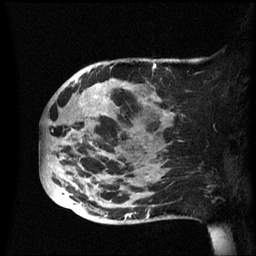
Breast MRI (dynamic contrast-enhanced), one sagittal slice; slice 22 of 60 in the series (ordered by position); dynamic contrast-enhanced series, image 2 of 3 at this slice position (ordered by acquisition); 1.5 T; TE 4.2 ms, TR 8.4 ms; 2.4 mm slice thickness; 256 × 256 image matrix. Patient: female, 49 years.
Structures marked on this image (semi-automatically segmented with operator editing):
- analysis volume of interest (the breast-tissue region the enhancement analysis was run in; not a lesion): bounding box <40,58,174,225> (left, top, right, bottom; pixels)
- tumour enhancement mask (voxels above the 70 % enhancement threshold inside the analysis volume of interest): <85,63,172,209>